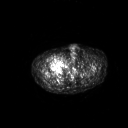
FDG PET of an extremity soft-tissue mass (from a PET/CT study), one axial slice. Slice 289 of 311 in the series (ordered by position). 128 × 128 image matrix. Male patient, age 50 years. Case-level facts recorded for this patient, not image findings: histological type: undifferentiated - pleiomorphic; grade: high; site of the primary tumour: right thigh.
Outlined on this slice (expert contour drawn on MRI and transferred to this co-registered scan by the dataset authors):
- gross tumour volume including surrounding oedema: bounding box <55,56,64,64> (left, top, right, bottom; pixels)
- gross tumour volume (mass): <56,58,62,63>